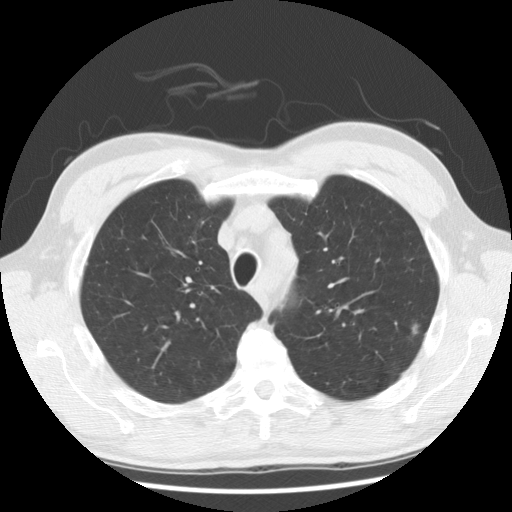
Low-dose screening chest CT, one axial slice. Position 117 of 148 along the scan axis. Reconstruction kernel STANDARD. Lung window (W 1500 / L -600 HU). 2.5 mm slice thickness. 512 × 512 image matrix.
Structures marked on this image (expert manual segmentation):
- lesion 1 (tumor, upper lobe of left lung): bounding box <410,322,421,335> (left, top, right, bottom; pixels)